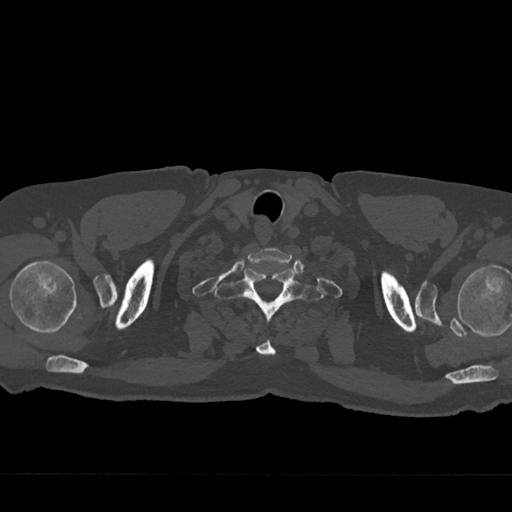
CT including the spine, one axial slice. Slice 666 of 797 in the series (ordered by position). 120 kVp. Bone window (W 1800 / L 400 HU). 0.5 mm slice thickness. 512 × 512 image matrix, field of view 377 × 377 mm. Male patient, age 75 years. Case-level facts recorded for this patient, not image findings: primary cancer: renal; vertebrae with lytic lesions (as recorded): T4.
Annotated regions visible in this slice (semi-automatically segmented with operator editing):
- T1 vertebra: bounding box (x1, y1, x2, y2) in pixels: (214, 268, 323, 355)